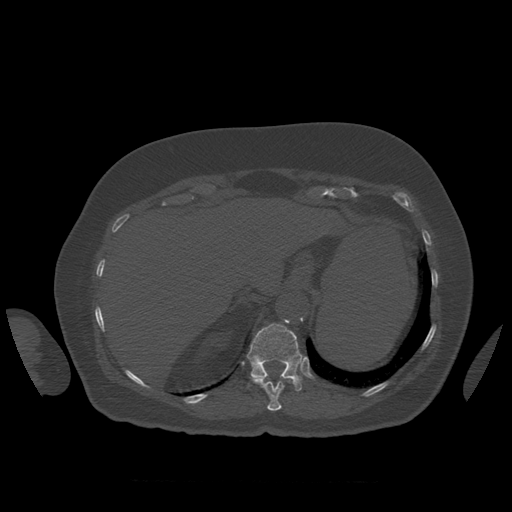
CT including the spine, one axial slice; position 309 of 399 along the scan axis; reconstruction kernel STANDARD; bone window (W 1800 / L 400 HU); 1.25 mm slice thickness; 512 × 512 image matrix, field of view 404 × 404 mm. Patient age 81 years. From the clinical record (not read from this slice): primary cancer: renal.
Annotated regions visible in this slice (semi-automatically segmented with operator editing):
- T11 vertebra: bounding box <251,378,285,411> (left, top, right, bottom; pixels)
- T12 vertebra: <247,324,303,392>